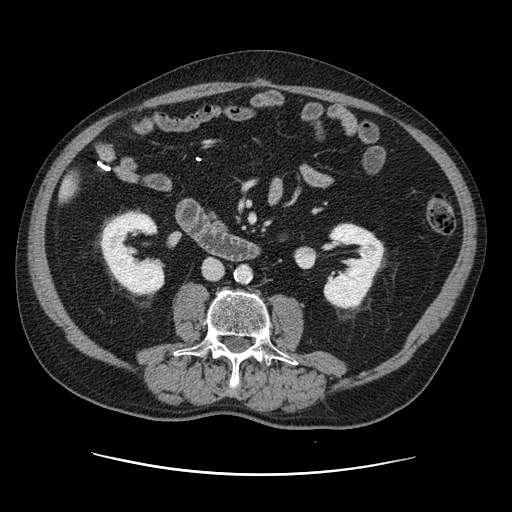
Contrast-enhanced abdominal CT, one axial slice. Slice 28 of 141 in the series (ordered by position). 120 kVp. Intravenous contrast given. Soft-tissue window (W 400 / L 40 HU). 512 × 512 image matrix, field of view 395 × 395 mm. Male patient, age 72 years. From the clinical record (not read from this slice): diagnosis: colorectal cancer liver metastases, imaged before liver resection; multiple liver metastases: yes; largest metastasis: 5.4 cm; disease in both lobes: yes.
Outlined on this slice (expert manual segmentation):
- liver: box from (x=64, y=185) to (x=70, y=195) px
- planned liver remnant (the part of the liver to remain after resection): (x=64, y=185)–(x=70, y=195)